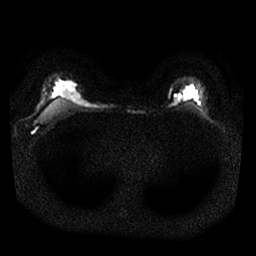
Breast MRI, one axial slice; slice 24 of 25 in the series (ordered by position); diffusion-weighted series; image 2 of 4 stored at this slice position (different b-values; order by instance number); 1.5 T; 4 mm slice thickness; 256 × 256 image matrix, field of view 320 × 320 mm. Female patient.
Structures marked on this image (expert manual segmentation):
- tumour on diffusion-weighted imaging: bounding box <176,96,180,101> (left, top, right, bottom; pixels)